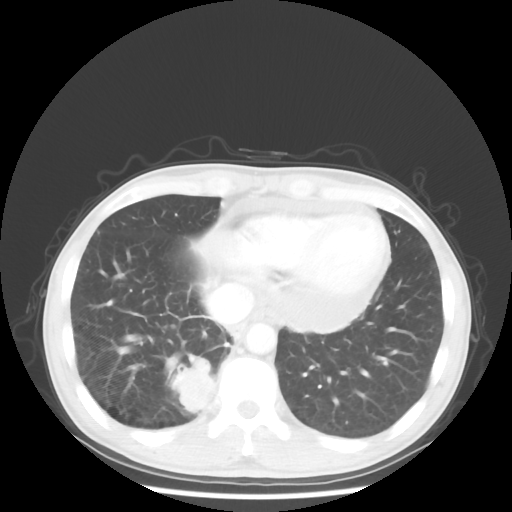
Chest CT, one axial slice; position 13 of 58 along the scan axis; reconstruction kernel STANDARD; 100 kVp; lung window (W 1500 / L -600 HU); 5 mm slice thickness; 512 × 512 image matrix, field of view 360 × 360 mm. Male patient, age 56 years. From the clinical record (not read from this slice): clinical TNM (as recorded): T2 N1 M1.
Annotated regions visible in this slice (bounding box drawn by a radiologist):
- lung tumour (recorded histology: adenocarcinoma): bounding box (x1, y1, x2, y2) in pixels: (170, 356, 216, 415)